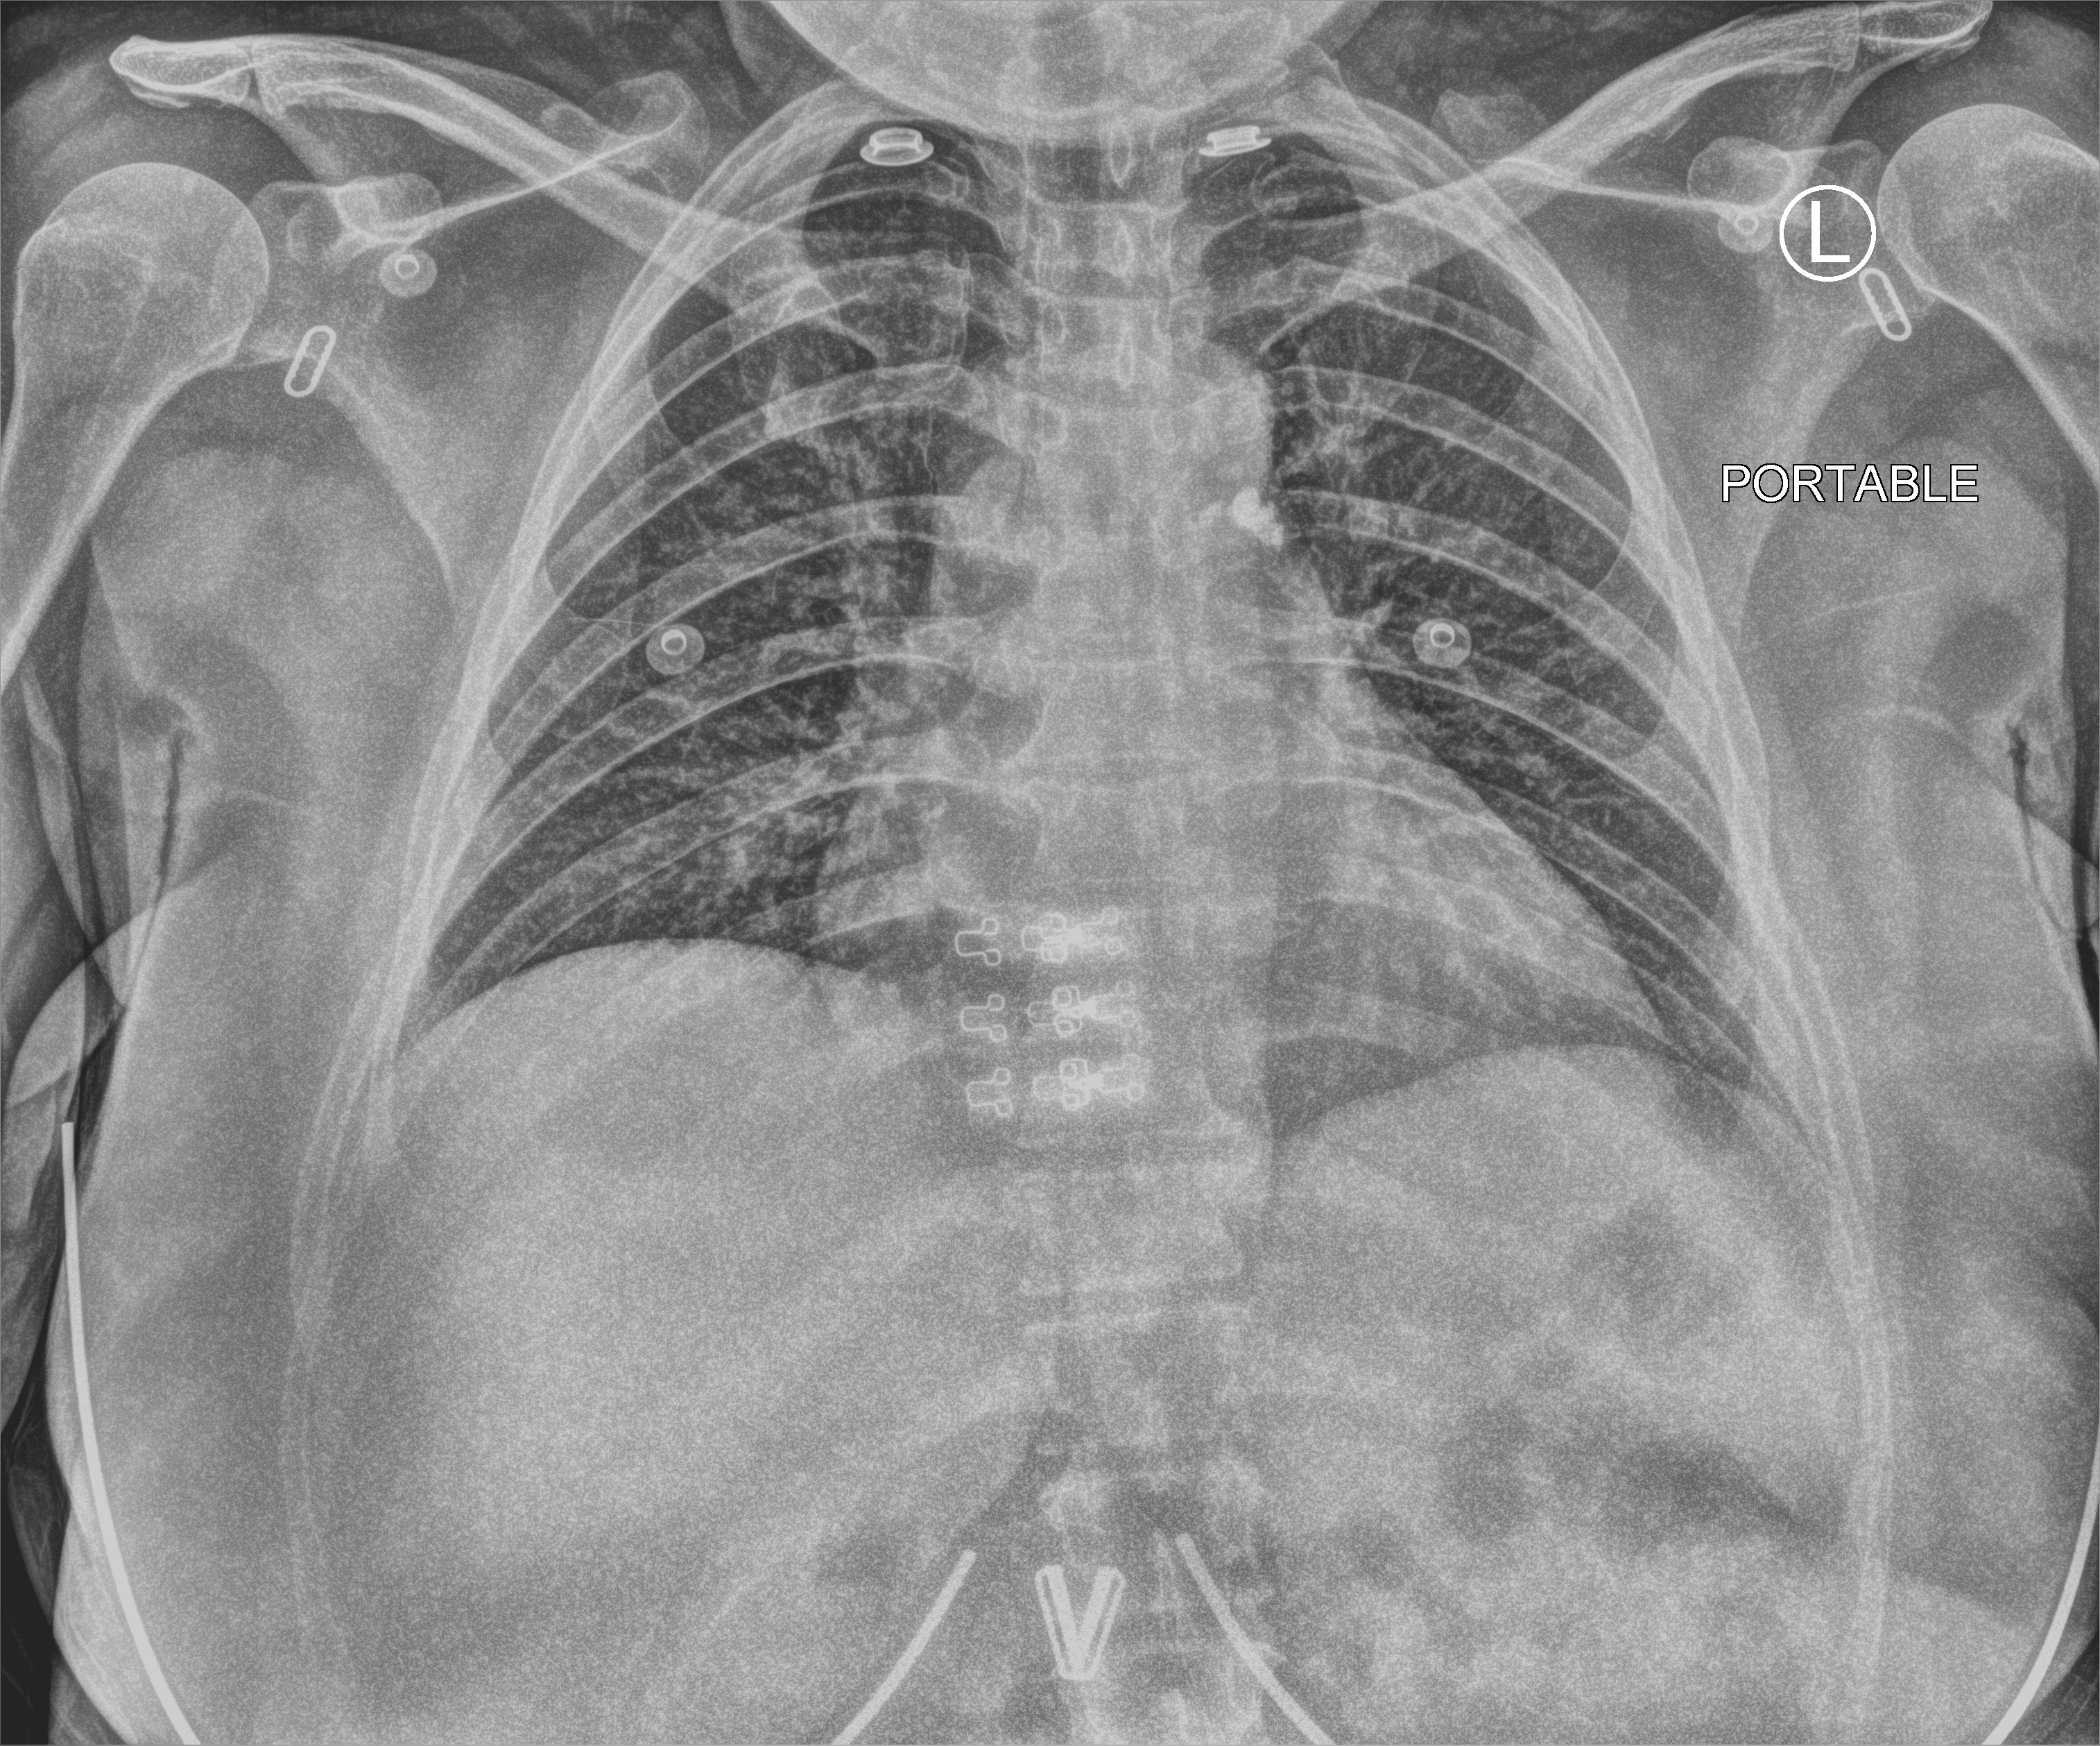
Portable chest radiograph; anteroposterior (AP) projection. Female patient hospitalised with COVID-19, age 18–59 years.
Hospital-stay facts (about this admission, not read from this image; timing relative to this image not recorded): mechanically ventilated during this hospital stay: no; other chronic lung disease (admission record): no; length of hospital stay: 2 days.